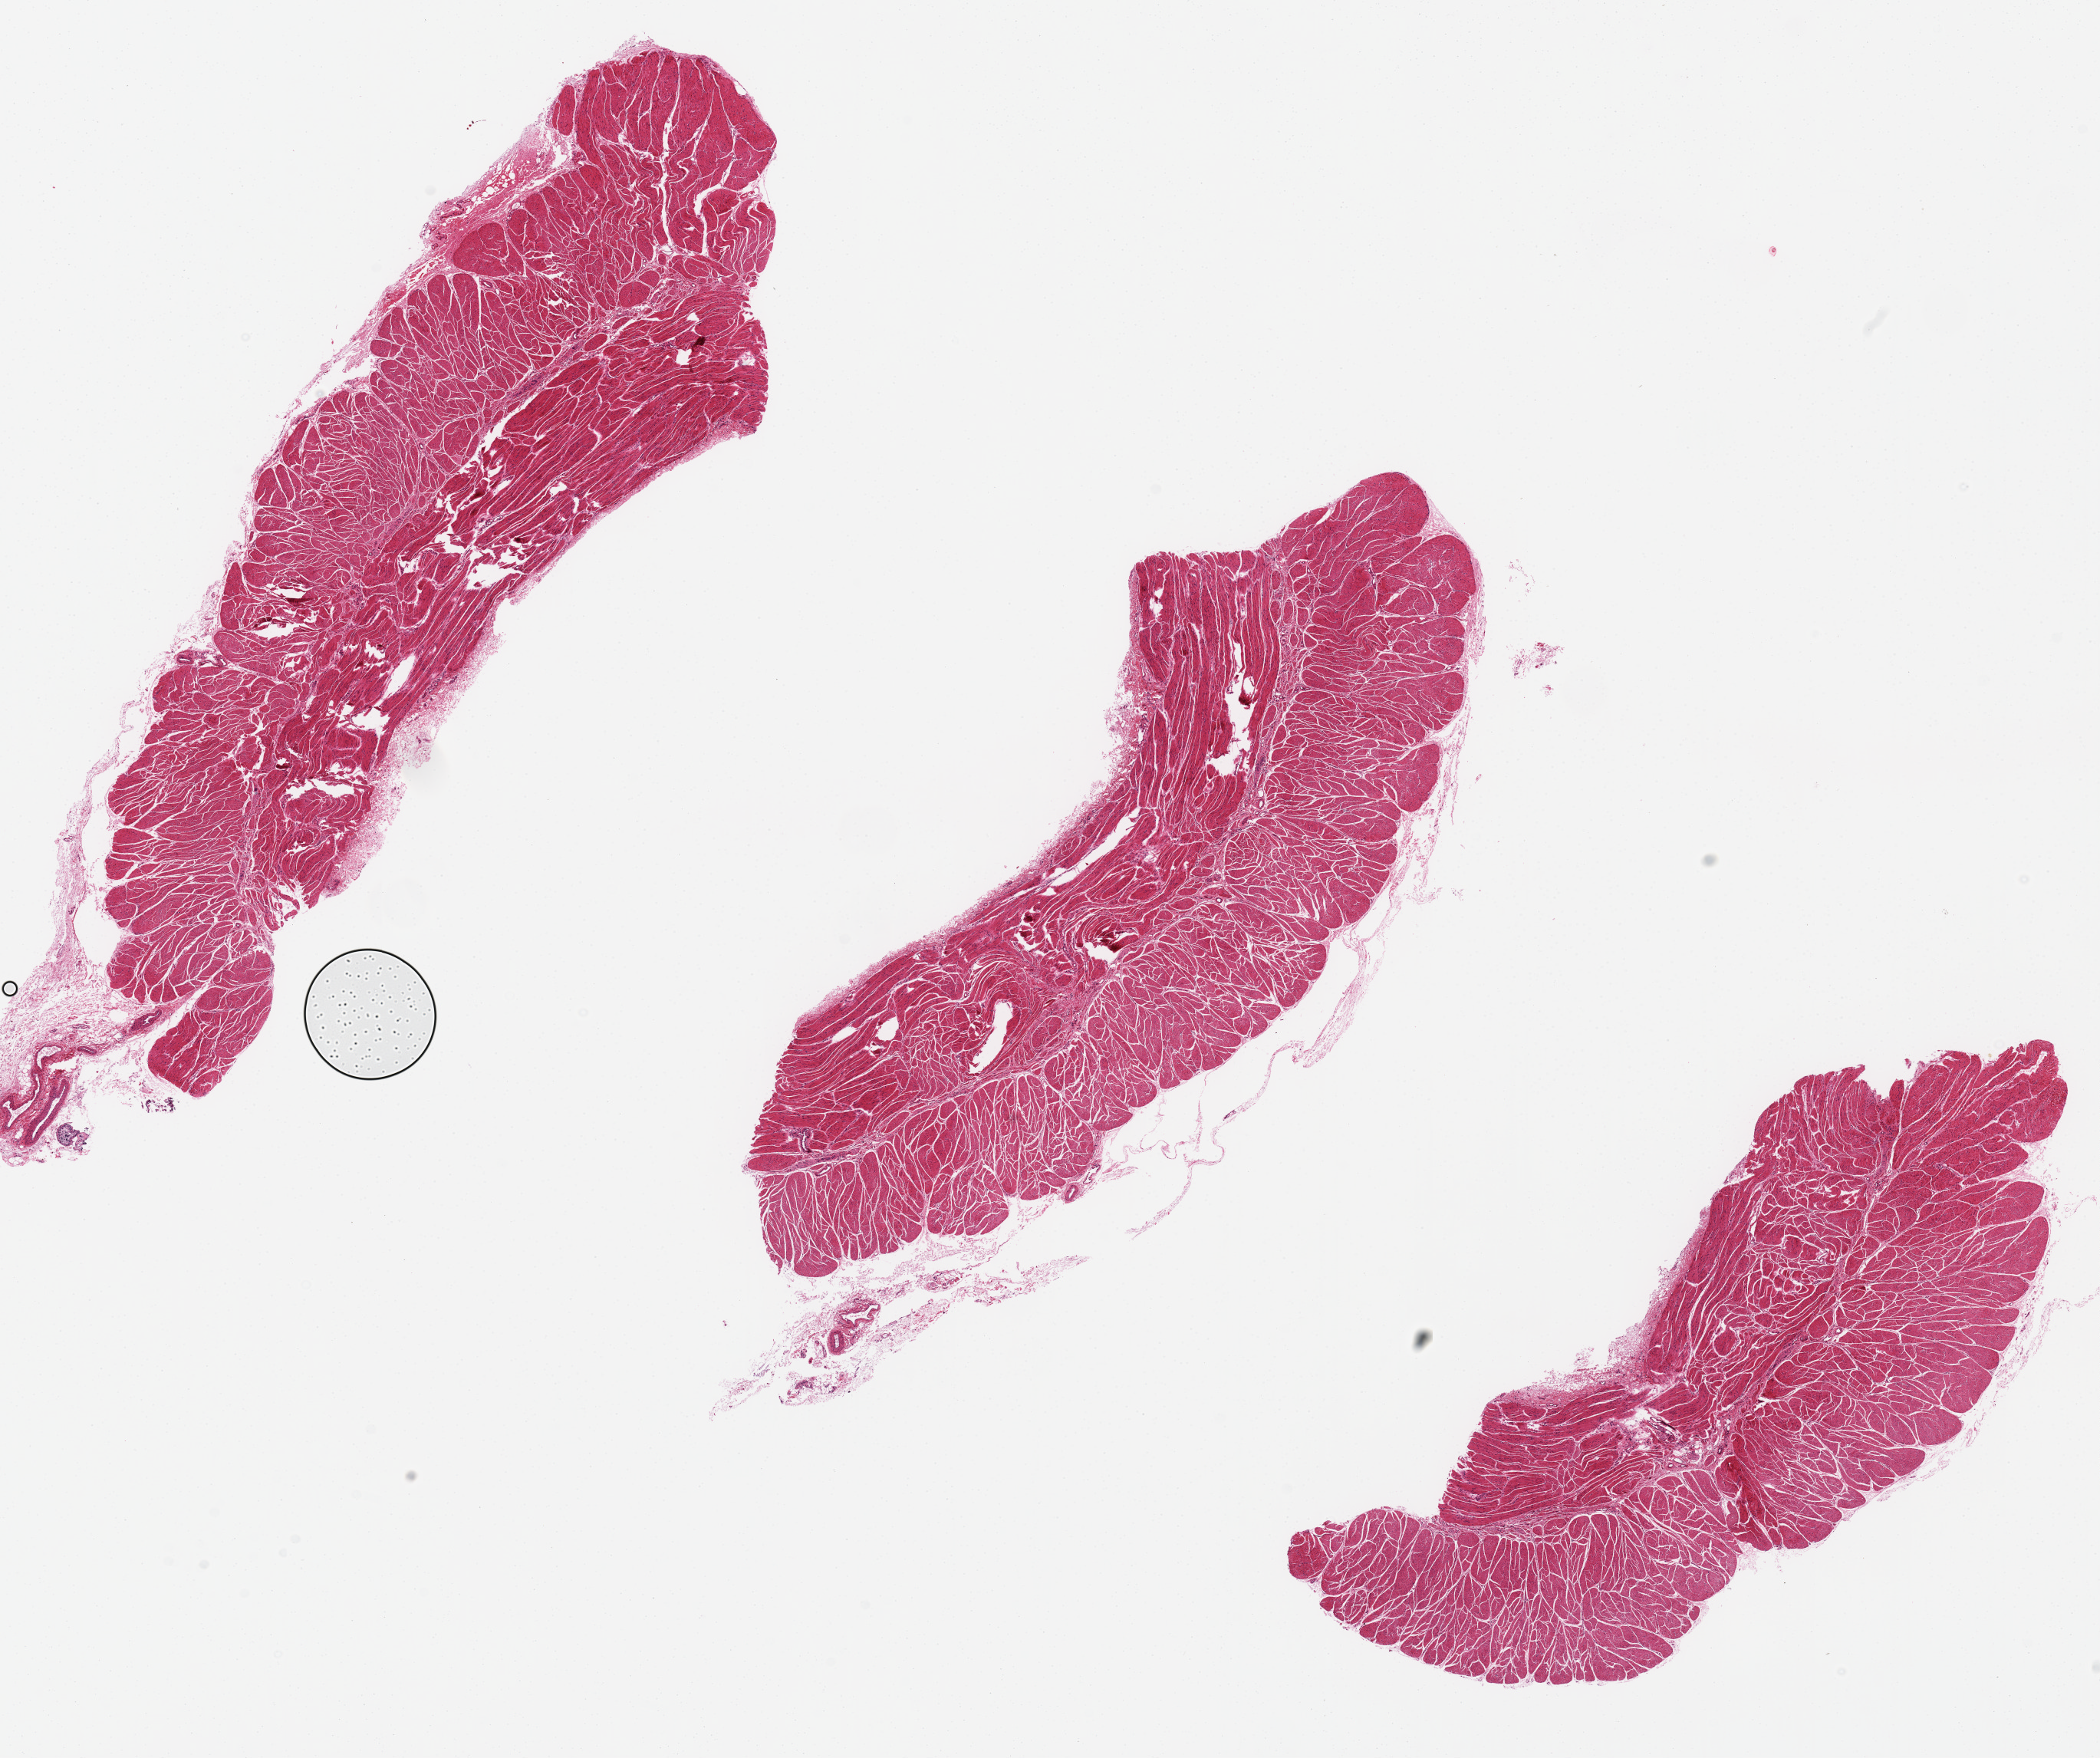
Digitized H&E-stained section, shown as a low-resolution overview of the whole scanned area (about 21.7 x 18.1 mm), PAXgene-fixed paraffin-embedded (PFPE) section, section of esophageal muscle (target tissue), donor tissue sample. Donor sex: male.
• reviewer comment on this tissue sample: 3 pieces: 13x3 mm